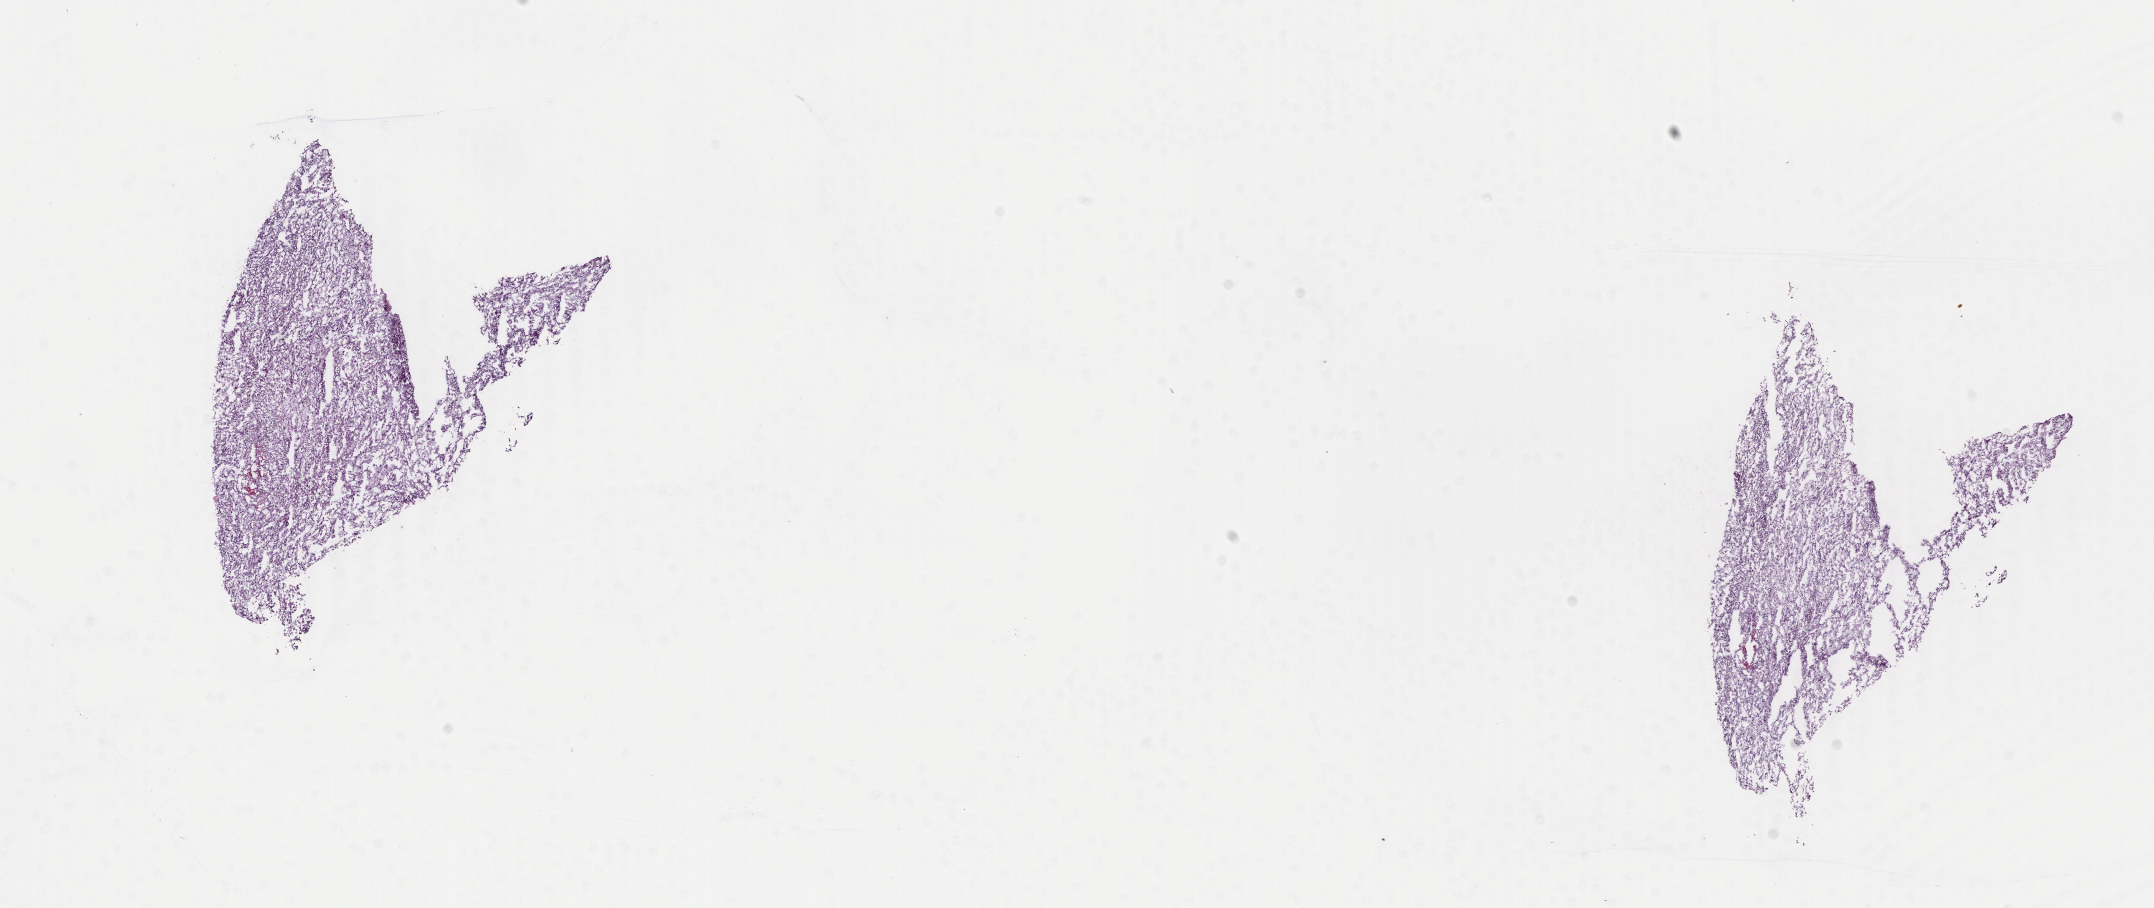
Digitized Hematoxylin and eosin (H&E) stained tissue section (whole slide), low-resolution overview of the scanned area, about 17.1 x 7.2 mm (from a 40x scan); frozen section from the top of the tissue portion; primary tumour sample from the kidney. Male, age 82 years at initial diagnosis. Slide review estimates, as recorded: tumour cells 98%, tumour nuclei 80%, normal cells 0%, stromal cells 0%, necrosis 2%. Inflammatory infiltration, as recorded: lymphocyte infiltration 2%, monocyte infiltration 3%, neutrophil infiltration 0%.
• diagnosis: Papillary adenocarcinoma, NOS
• laterality: right